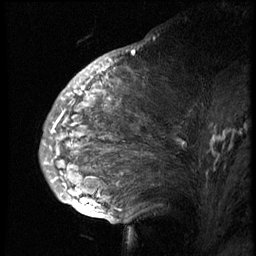
Breast MRI (dynamic contrast-enhanced), one sagittal slice; 3 images stored at this slice position (order not interpretable as contrast timing); 1.5 T; TE 4.2 ms, TR 8.9 ms; 2.5 mm slice thickness; 256 × 256 image matrix, field of view 200 × 200 mm. Patient: female, 57 years. Case-level facts recorded for this patient, not image findings: setting: breast cancer imaged before/during neoadjuvant chemotherapy; receptor status: HER2-positive.
Structures marked on this image (semi-automatically segmented with operator editing):
- analysis volume of interest (the breast-tissue region the enhancement analysis was run in; not a lesion): bounding box <51,67,249,173> (left, top, right, bottom; pixels)
- tumour enhancement mask (voxels above the 140 % enhancement threshold inside the analysis volume of interest): <64,99,219,140>